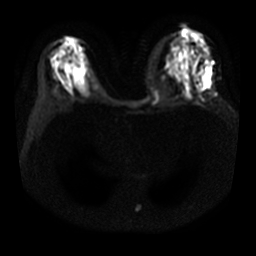
Breast MRI, one axial slice; position 15 of 29 along the scan axis; diffusion-weighted series; image 2 of 4 stored at this slice position (different b-values; order by instance number); 3 T; 5 mm slice thickness; 256 × 256 image matrix. Female patient.
Structures marked on this image (expert manual segmentation):
- tumour on diffusion-weighted imaging: bounding box [x1, y1, x2, y2] px = [201, 74, 208, 84]